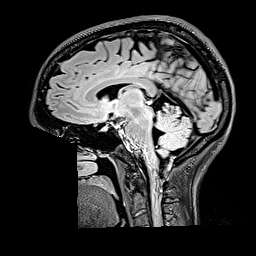
Brain MRI from a brain-tumour surgery series, one sagittal slice; position 84 of 176 along the scan axis; T2 FLAIR; 256 × 256 image matrix, field of view 256 × 256 mm. Case-level facts recorded for this patient, not image findings: histopathology: Oligodendroglioma; WHO grade: 2; IDH mutation: yes; tumour location: Right Parietal.
Structures marked on this image (expert manual segmentation):
- tumour: bounding box (x1, y1, x2, y2) in pixels: (180, 77, 187, 82)